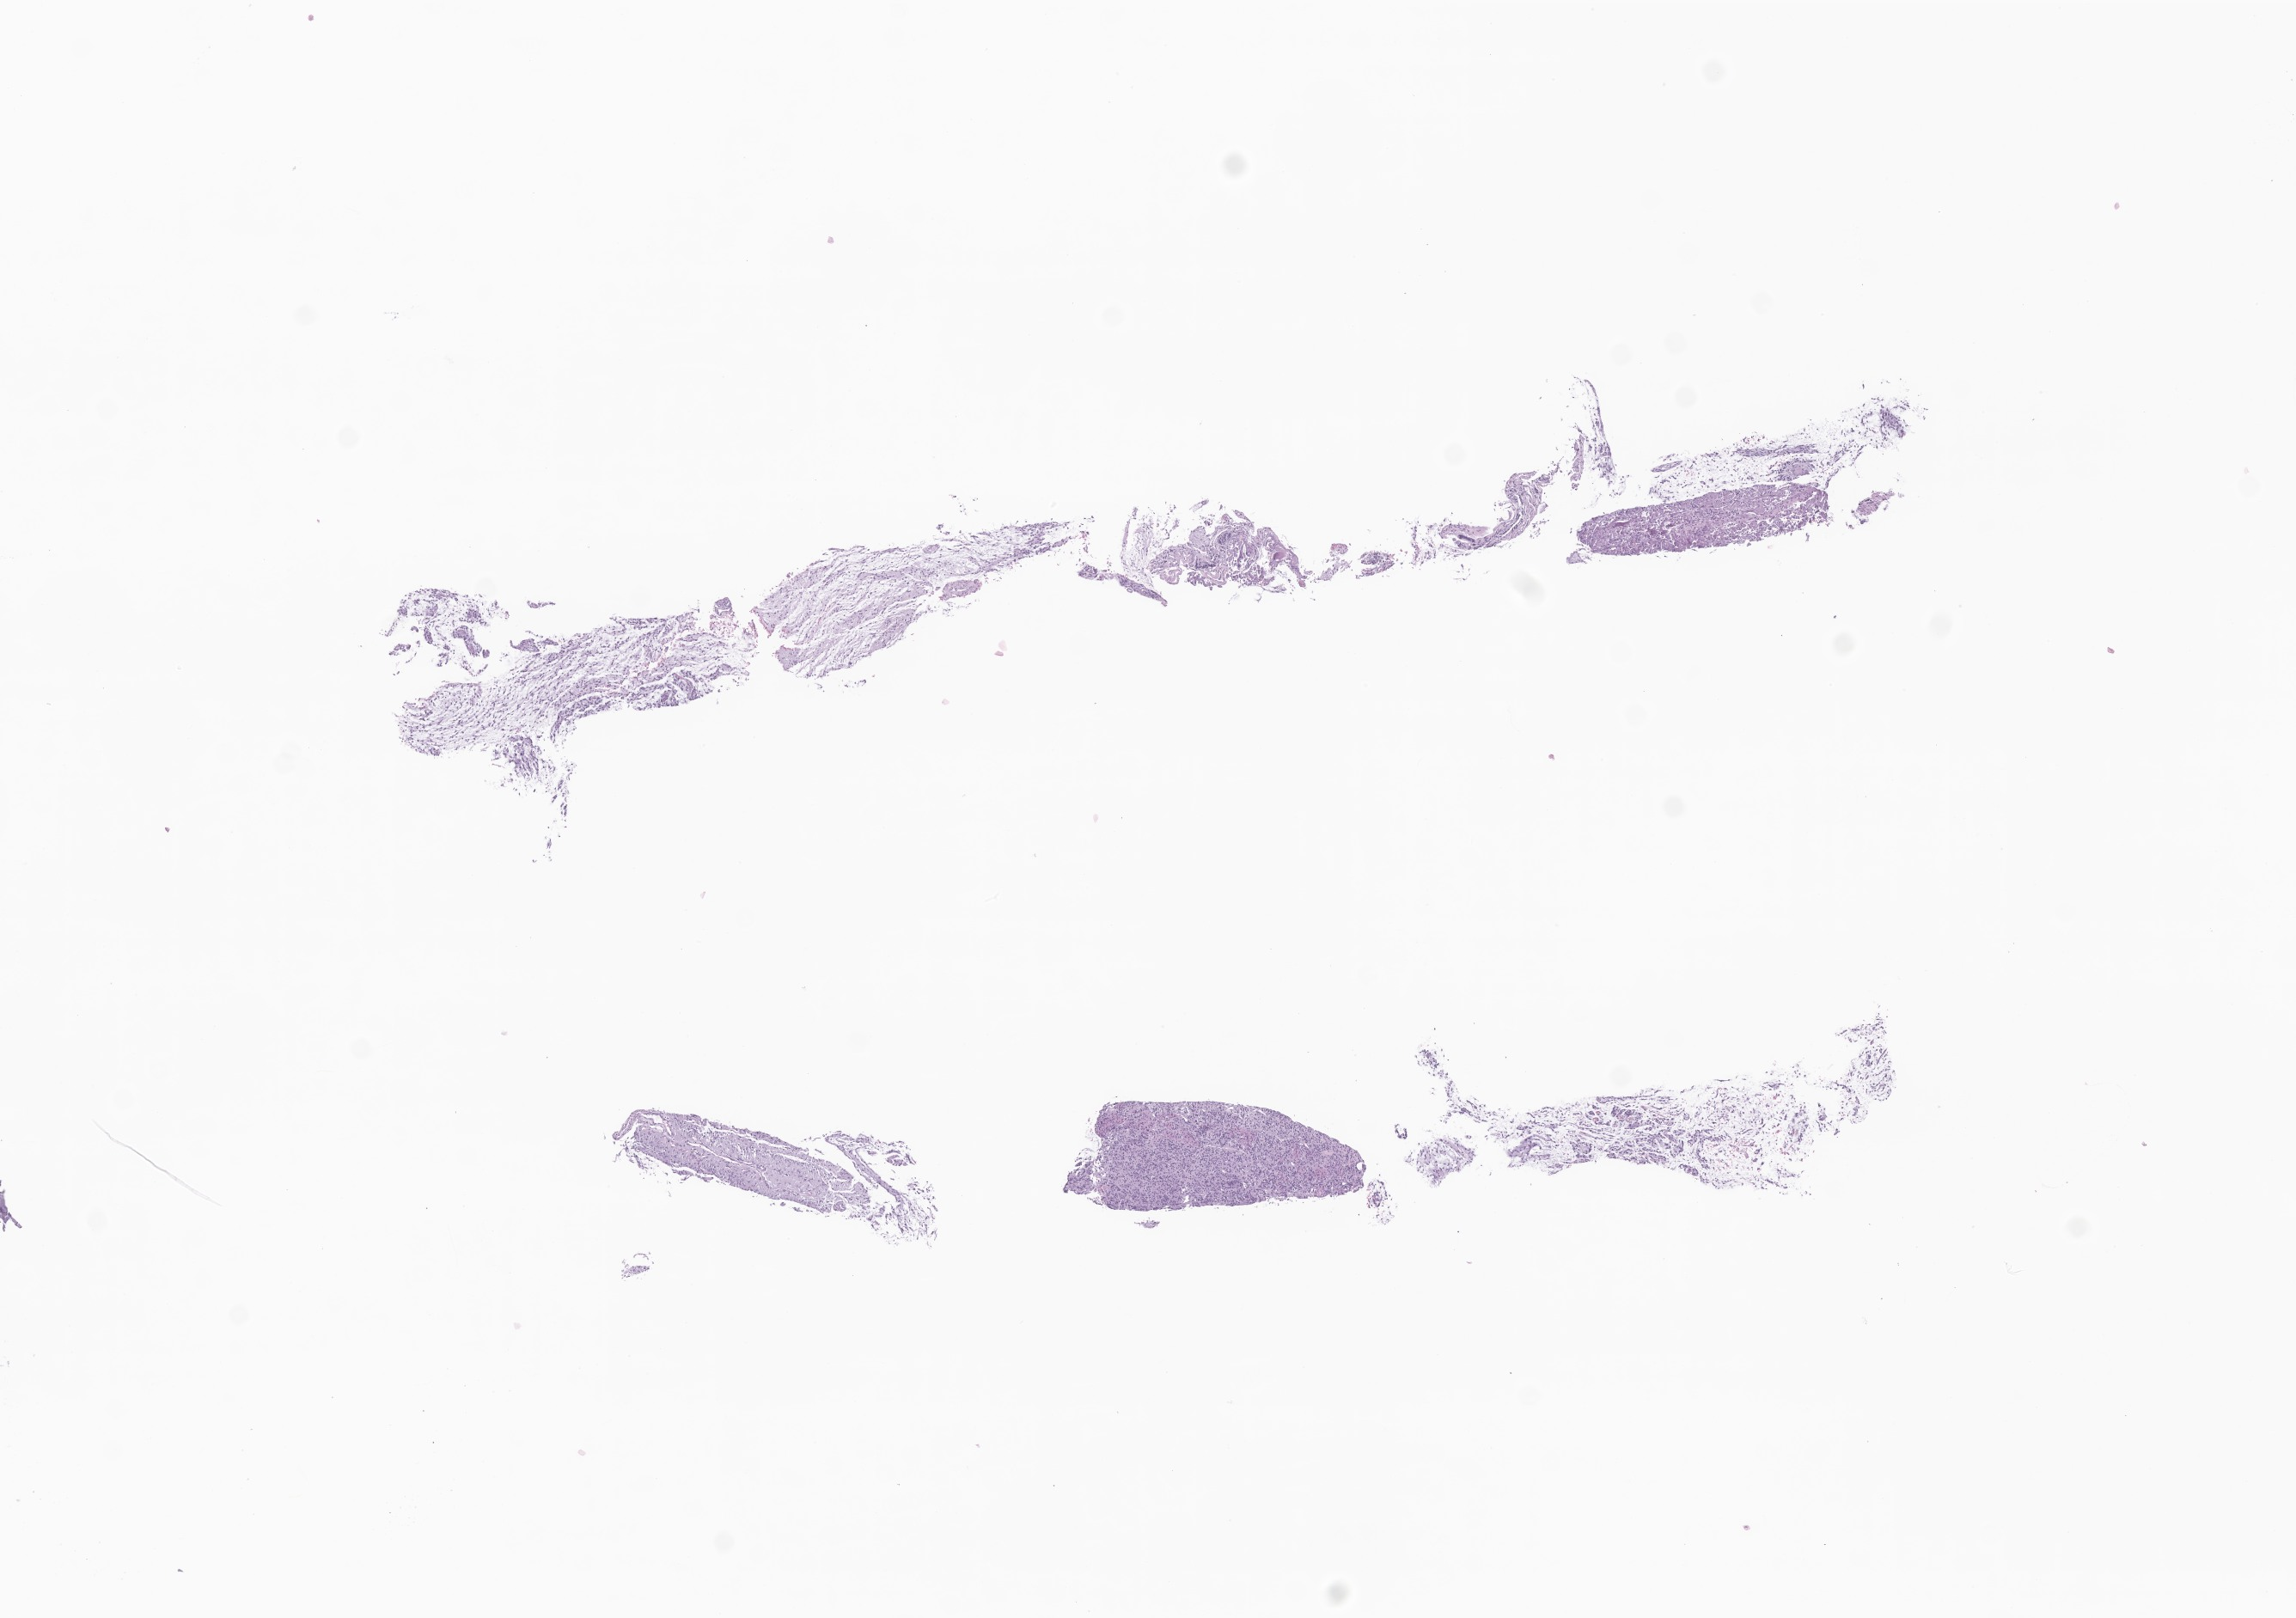
Digitized haematoxylin and eosin-stained section of tumor tissue from the brain, low-resolution overview of the scanned area, about 11.3 x 7.9 mm. Formalin-fixed paraffin-embedded section. Male patient, age 80 months (6 years 8 months).
Diagnosis: Pilocytic astrocytoma.